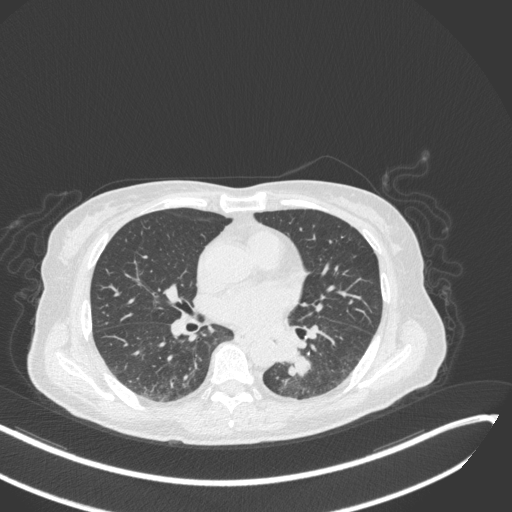
Chest CT, one axial slice. Position 131 of 342 along the scan axis. Reconstruction kernel B31f. 120 kVp. Lung window (W 1500 / L -600 HU). 512 × 512 image matrix, field of view 400 × 400 mm. Patient: female, 64 years. Case-level facts recorded for this patient, not image findings: clinical TNM (as recorded): T3 N1 M1.
Outlined on this slice (bounding box drawn by a radiologist):
- lung tumour (recorded histology: small cell carcinoma): bounding box [x1, y1, x2, y2] px = [273, 338, 314, 381]